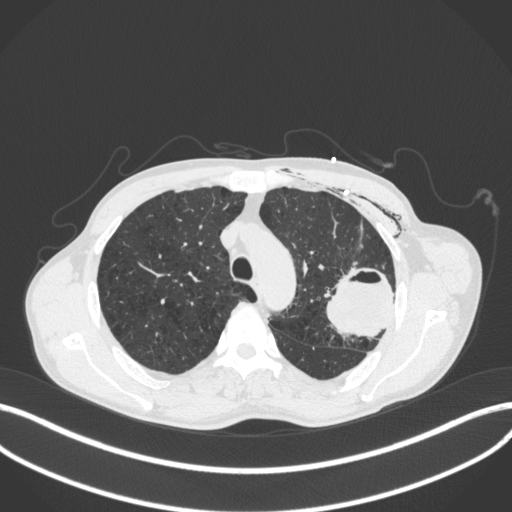
Chest CT, one axial slice. 120 kVp. Lung window (W 1500 / L -600 HU). 1 mm slice thickness. 512 × 512 image matrix, field of view 400 × 400 mm. Patient: male, 58 years. Case-level facts recorded for this patient, not image findings: clinical TNM (as recorded): T3 N0 M0.
Outlined on this slice (rectangle marked by the reading radiologist):
- lung tumour (recorded histology: adenocarcinoma): box from (x=319, y=260) to (x=398, y=341) px